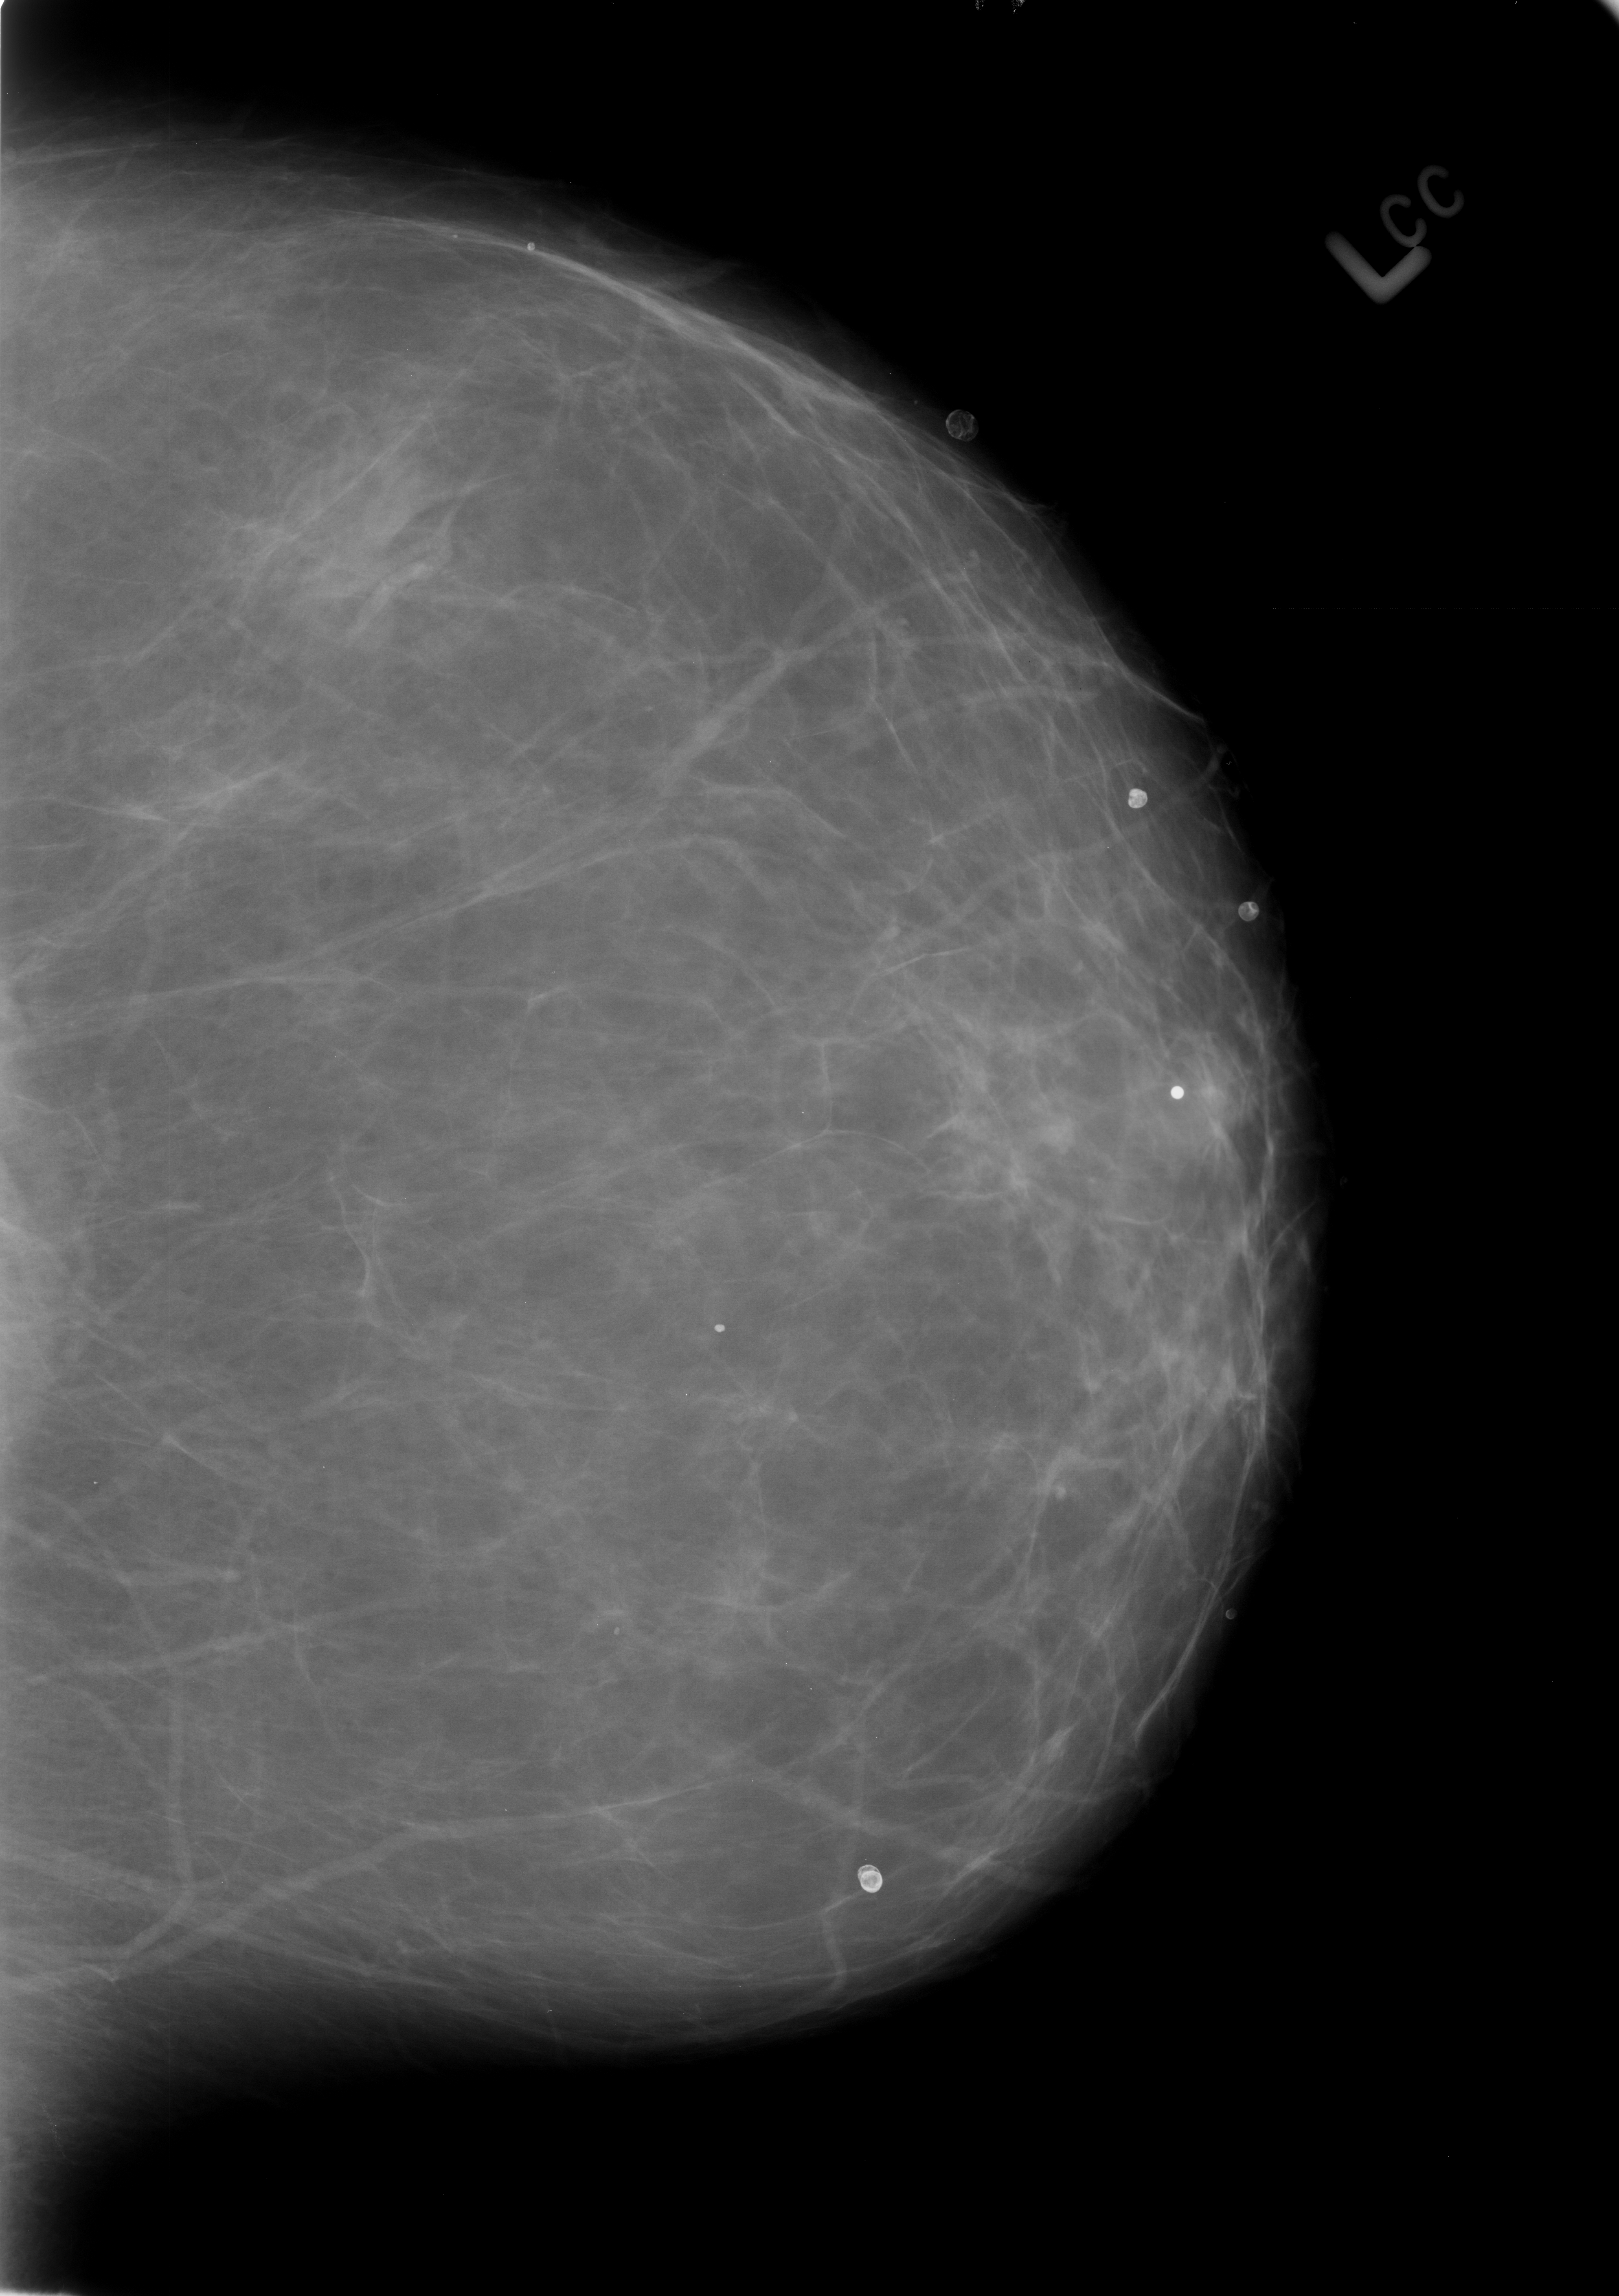
Digitized screen-film mammogram, left breast, craniocaudal (CC) view.
- Radiologist-marked abnormalities on this image: Finding 1 of 5: calcifications, morphology eggshell; BI-RADS assessment category 2; benign without callback (not worked up further).
- Finding 2 of 5: calcifications, morphology lucent center; BI-RADS assessment category 2; benign without callback (not worked up further).
- Finding 3 of 5: calcifications, morphology lucent center; BI-RADS assessment category 2; benign without callback (not worked up further).
- Finding 4 of 5: calcifications, morphology lucent center; BI-RADS assessment category 2; benign without callback (not worked up further).
- Finding 5 of 5: calcifications, morphology lucent center; BI-RADS assessment category 2; benign without callback (not worked up further).